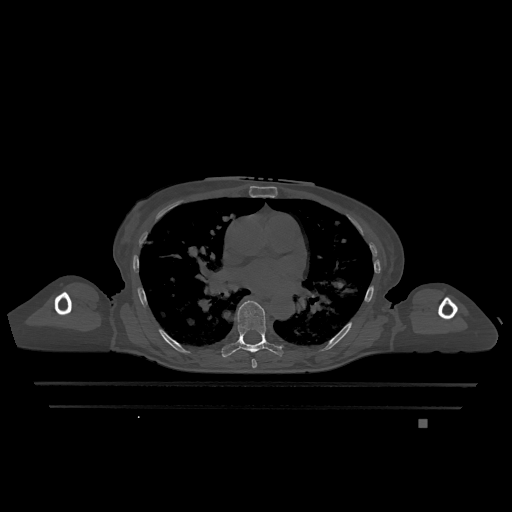
CT including the spine, one axial slice. Position 743 of 1317 along the scan axis. Bone window (W 1800 / L 400 HU). 0.5 mm slice thickness. 512 × 512 image matrix, field of view 500 × 500 mm. Patient: female, 74 years. Case-level facts recorded for this patient, not image findings: primary cancer: lung.
Outlined on this slice (semi-automatically segmented with operator editing):
- T6 vertebra: box from (x=252, y=359) to (x=257, y=368) px
- T7 vertebra: (x=221, y=300)–(x=283, y=358)